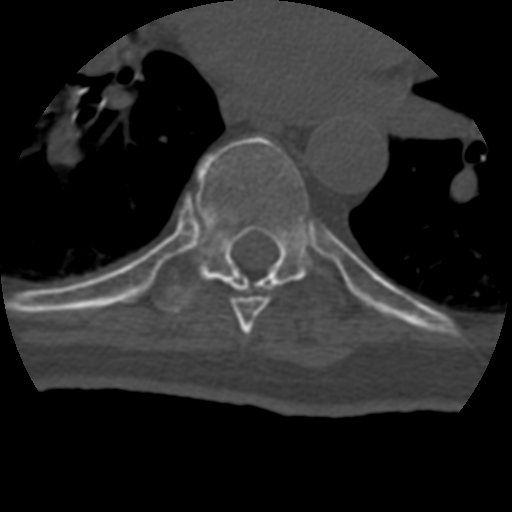
CT including the spine, one axial slice. 120 kVp. Bone window (W 1800 / L 400 HU). 1.25 mm slice thickness. 512 × 512 image matrix, field of view 160 × 160 mm. Patient age 69 years. Case-level facts recorded for this patient, not image findings: primary cancer: prostate.
Structures marked on this image (semi-automatically segmented with operator editing):
- T7 vertebra: bounding box (x1, y1, x2, y2) in pixels: (232, 296, 269, 335)
- T8 vertebra: (155, 136, 344, 316)